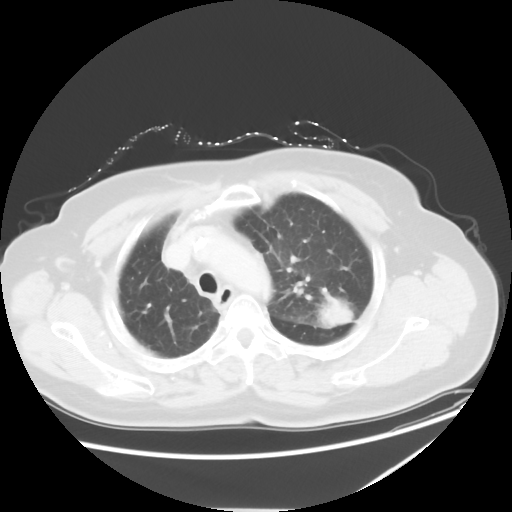
Chest CT, one axial slice. Position 42 of 54 along the scan axis. Lung window (W 1500 / L -600 HU). 5 mm slice thickness. 512 × 512 image matrix, field of view 384 × 384 mm. Female patient, age 61 years. From the clinical record (not read from this slice): clinical TNM (as recorded): T1c N3 M1.
Structures marked on this image (bounding box drawn by a radiologist):
- lung tumour (recorded histology: adenocarcinoma): bounding box [x1, y1, x2, y2] px = [311, 293, 362, 335]